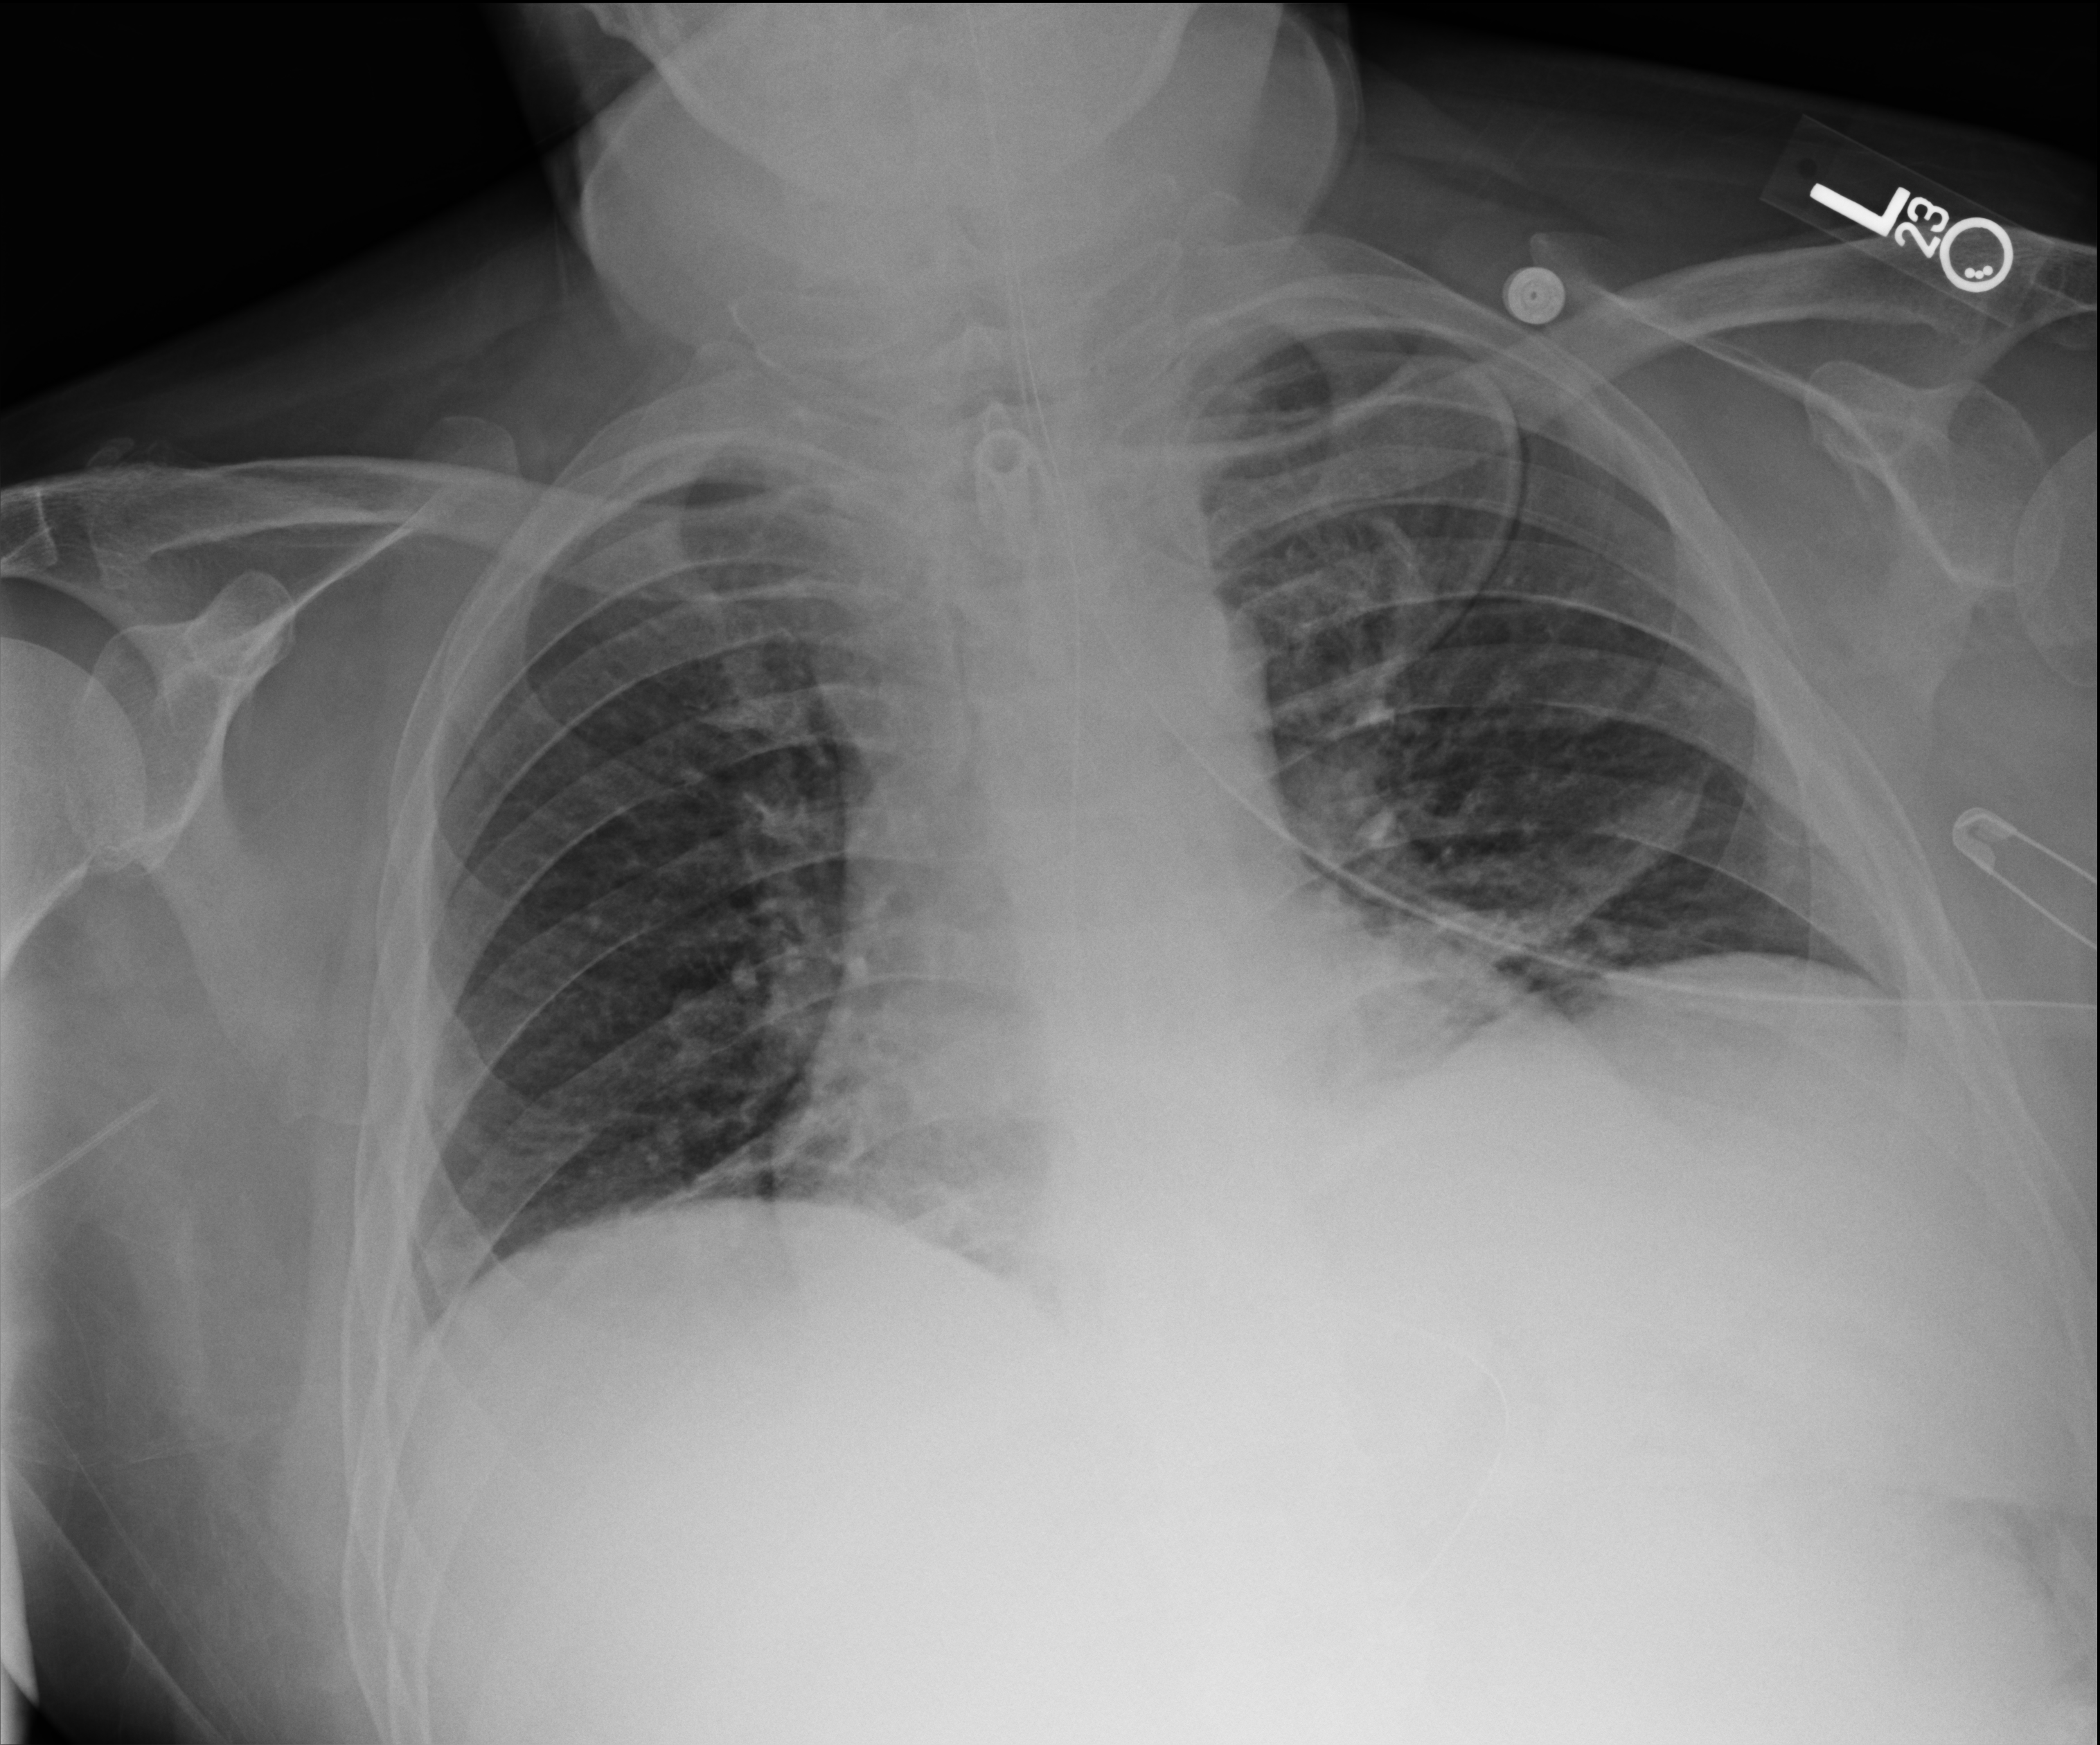
Portable chest radiograph. Male patient hospitalised with COVID-19, age 18–59 years.
From the hospital-stay record, not from the radiograph (when in the stay this image was taken is not recorded):
- admitted to intensive care during this hospital stay: yes